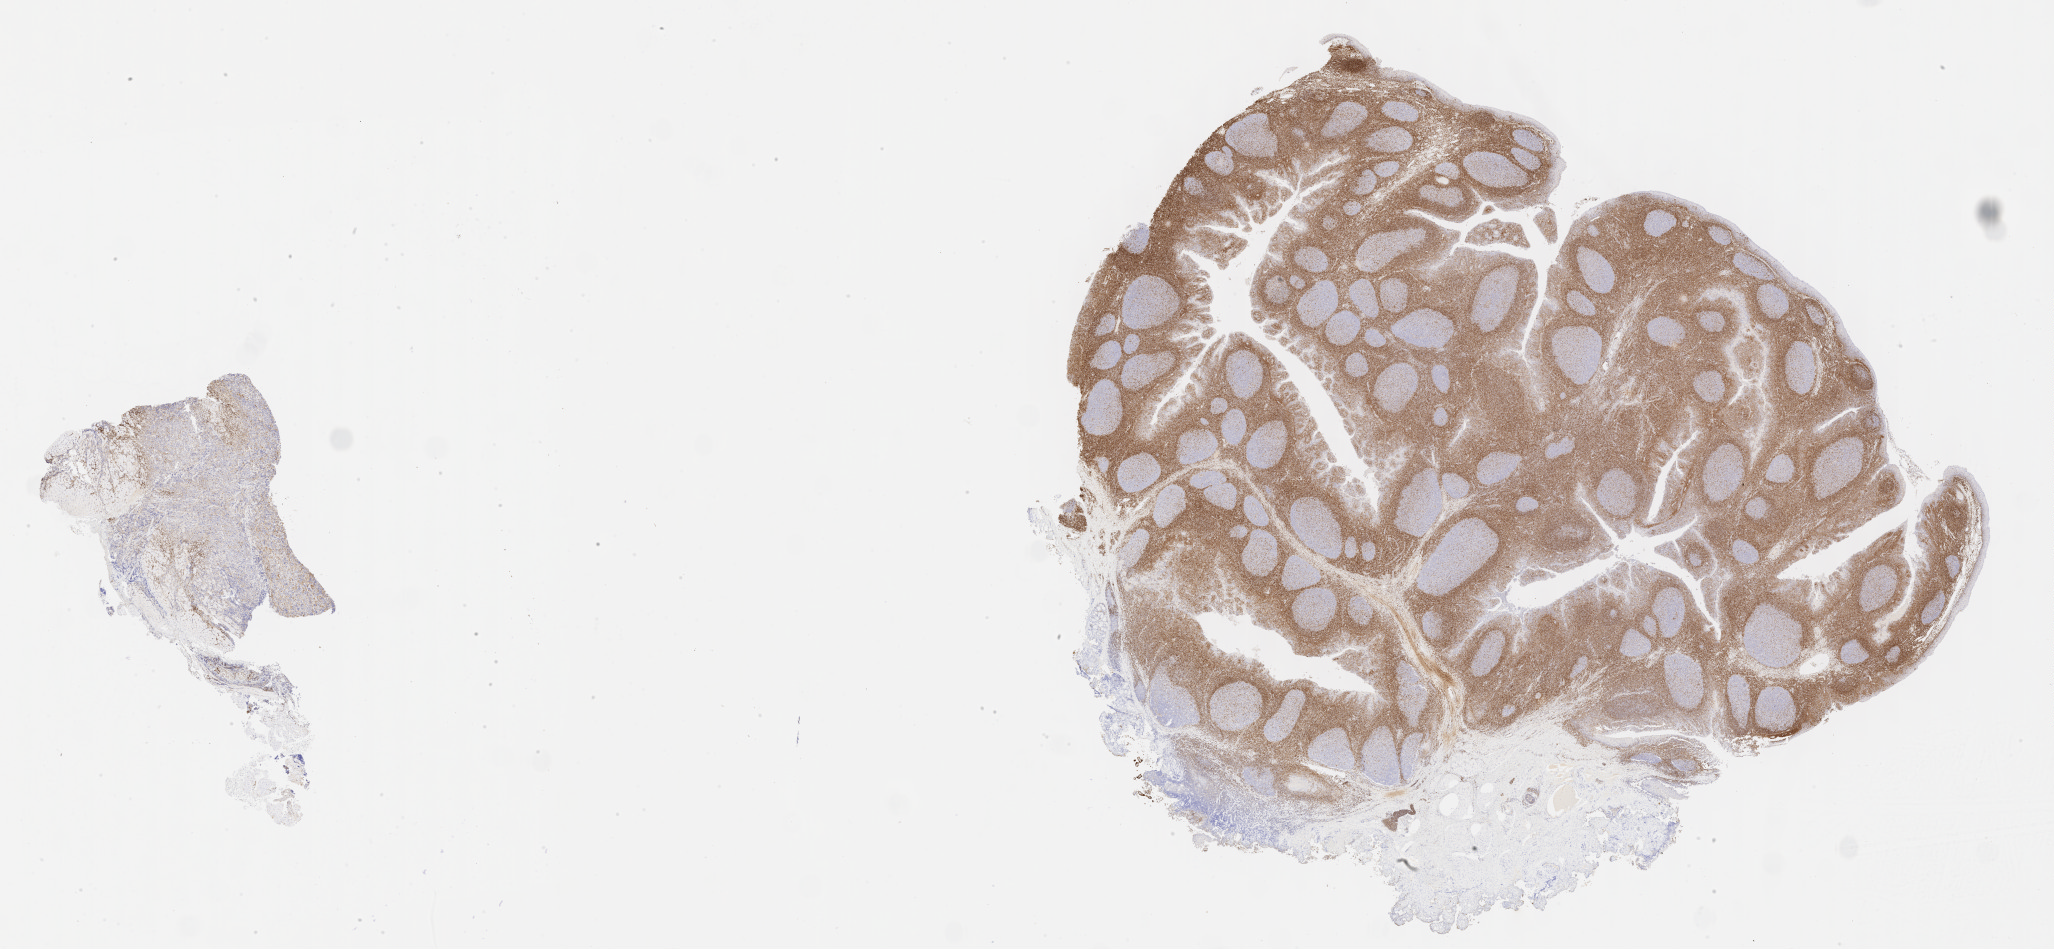
Whole-slide image, immunohistochemical stain for BCL2, low-resolution overview of the scanned area, about 33.2 x 15.3 mm, tumor tissue, site: kidney. Male patient, 12 years old.
• diagnosis: Diffuse large B-cell lymphoma, NOS